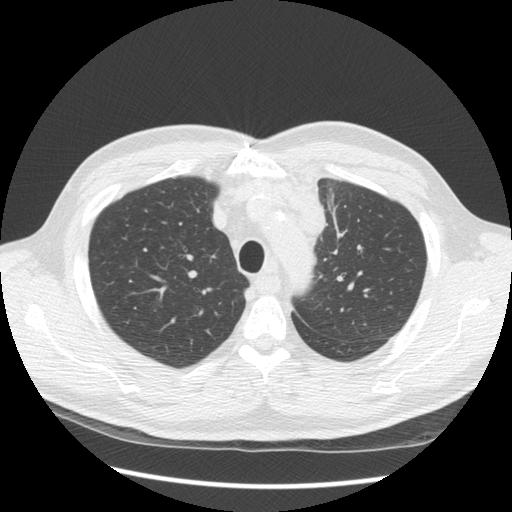
Low-dose screening chest CT, one axial slice; slice 108 of 136 in the series (ordered by position); 120 kVp; lung window (W 1500 / L -600 HU); 2.5 mm slice thickness; 512 × 512 image matrix, field of view 360 × 360 mm.
Outlined on this slice (expert manual segmentation):
- lesion 1 (tumor, upper lobe of left lung): box from (x=282, y=179) to (x=326, y=245) px